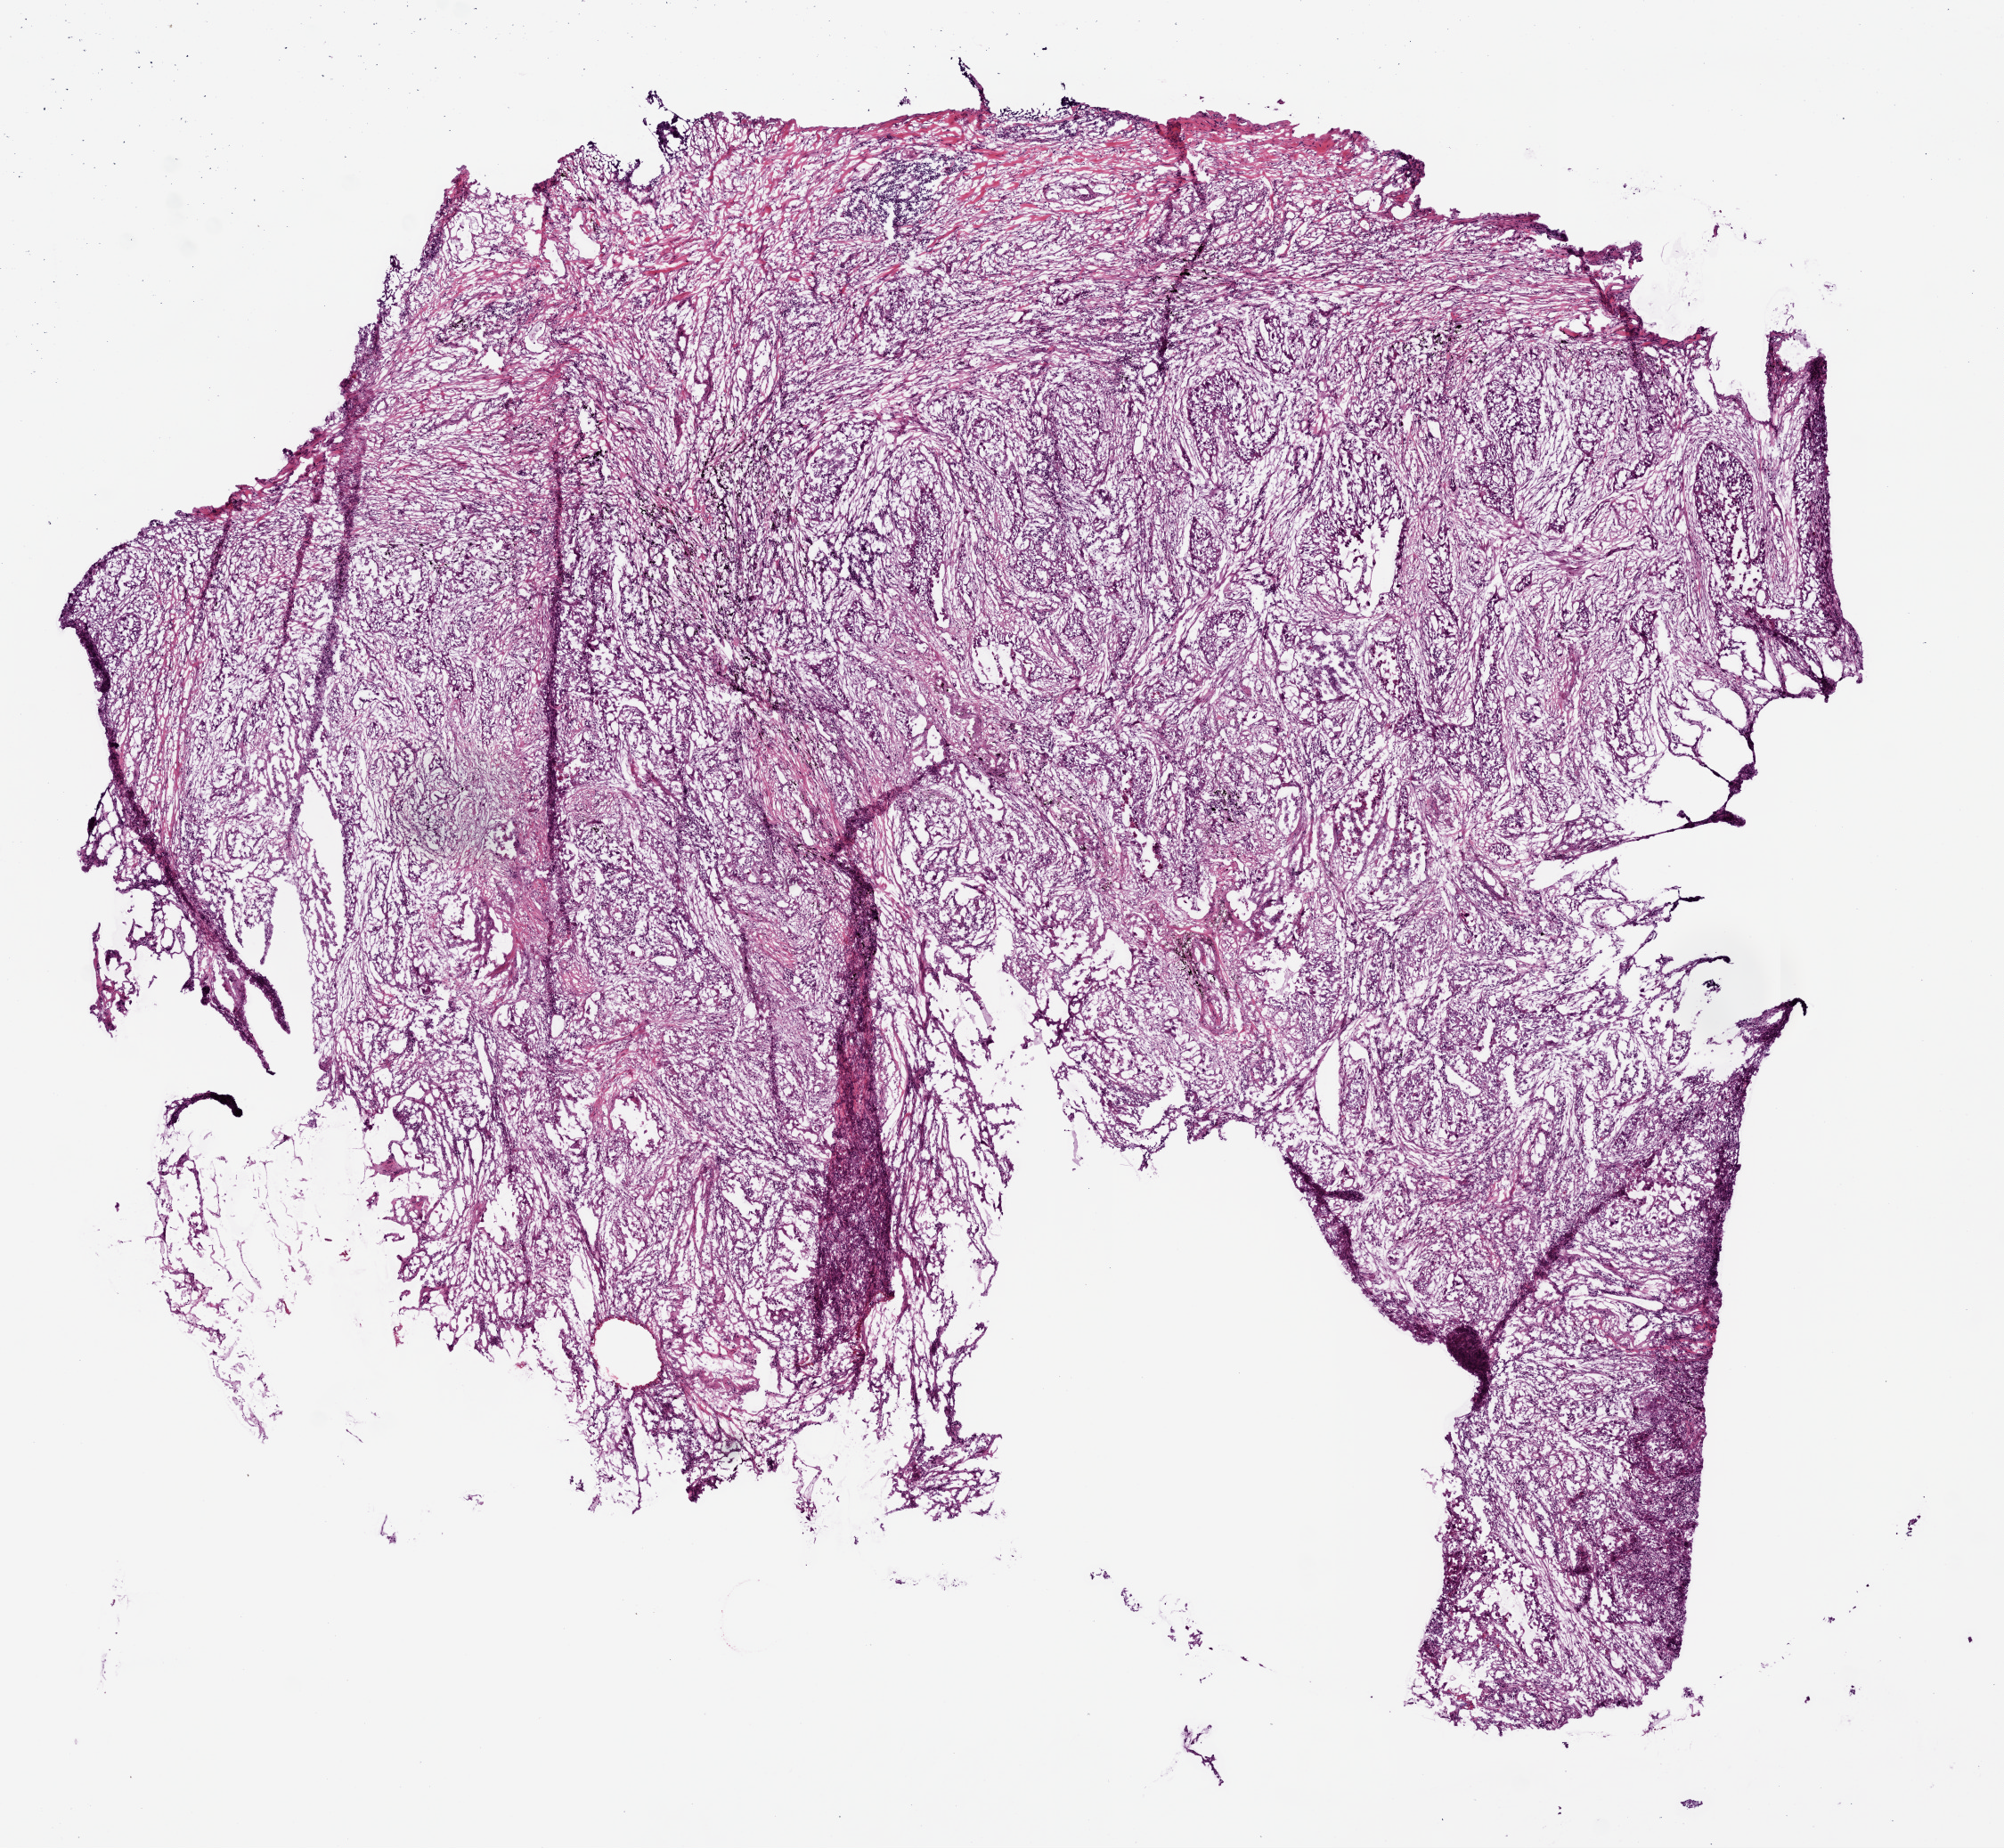
Whole-slide histology image, H&E — low-resolution overview of the scanned area, about 9.0 x 8.3 mm. Frozen section from the top of the tissue portion. Primary tumour sample from the lung. Male, age 70 years at initial diagnosis. Pathologist review of this section (percent, as recorded): tumour cells 100%, tumour nuclei 65%, normal cells 0%, stromal cells 0%, necrosis 0%. Inflammatory infiltration, as recorded: lymphocyte infiltration 20%, monocyte infiltration 2%, neutrophil infiltration 10%.
- pathologic diagnosis: Squamous cell carcinoma, NOS
- TNM: T3 N0 M0
- laterality: left
- AJCC pathologic stage: IIB